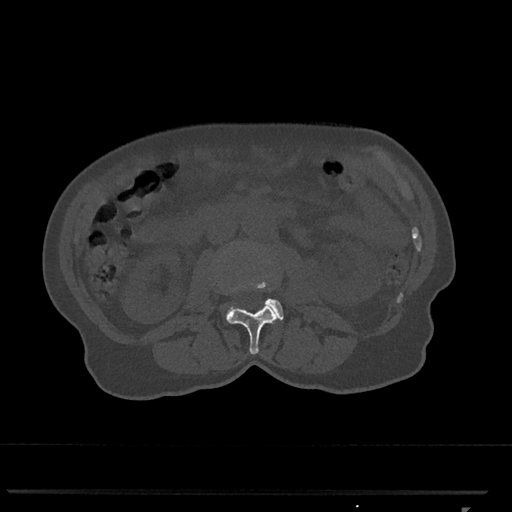
CT including the spine, one axial slice; slice 310 of 793 in the series (ordered by position); reconstruction kernel Br40s/3; 120 kVp; bone window (W 1800 / L 400 HU); 0.5 mm slice thickness; 512 × 512 image matrix. Patient: female, 62 years. Case-level facts recorded for this patient, not image findings: primary cancer: renal.
Structures marked on this image (semi-automatically segmented with operator editing):
- L2 vertebra: bounding box (x1, y1, x2, y2) in pixels: (226, 303, 278, 354)
- L3 vertebra: (226, 281, 284, 321)